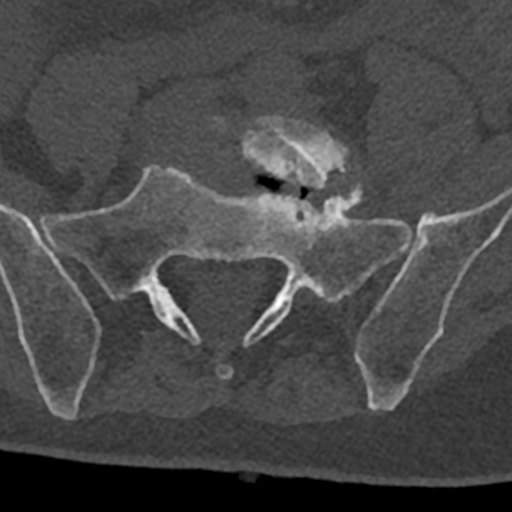
CT including the spine, one axial slice. Slice 156 of 797 in the series (ordered by position). Bone window (W 1800 / L 400 HU). 0.5 mm slice thickness. 512 × 512 image matrix, field of view 160 × 160 mm. Male patient, age 74 years. Case-level facts recorded for this patient, not image findings: primary cancer: renal; vertebrae with lytic lesions (as recorded): T10, L1, L2, L3, L4, L5.
Structures marked on this image (semi-automatic segmentation, software-assisted and operator-edited):
- L5 vertebra: bounding box <216,115,348,189> (left, top, right, bottom; pixels)